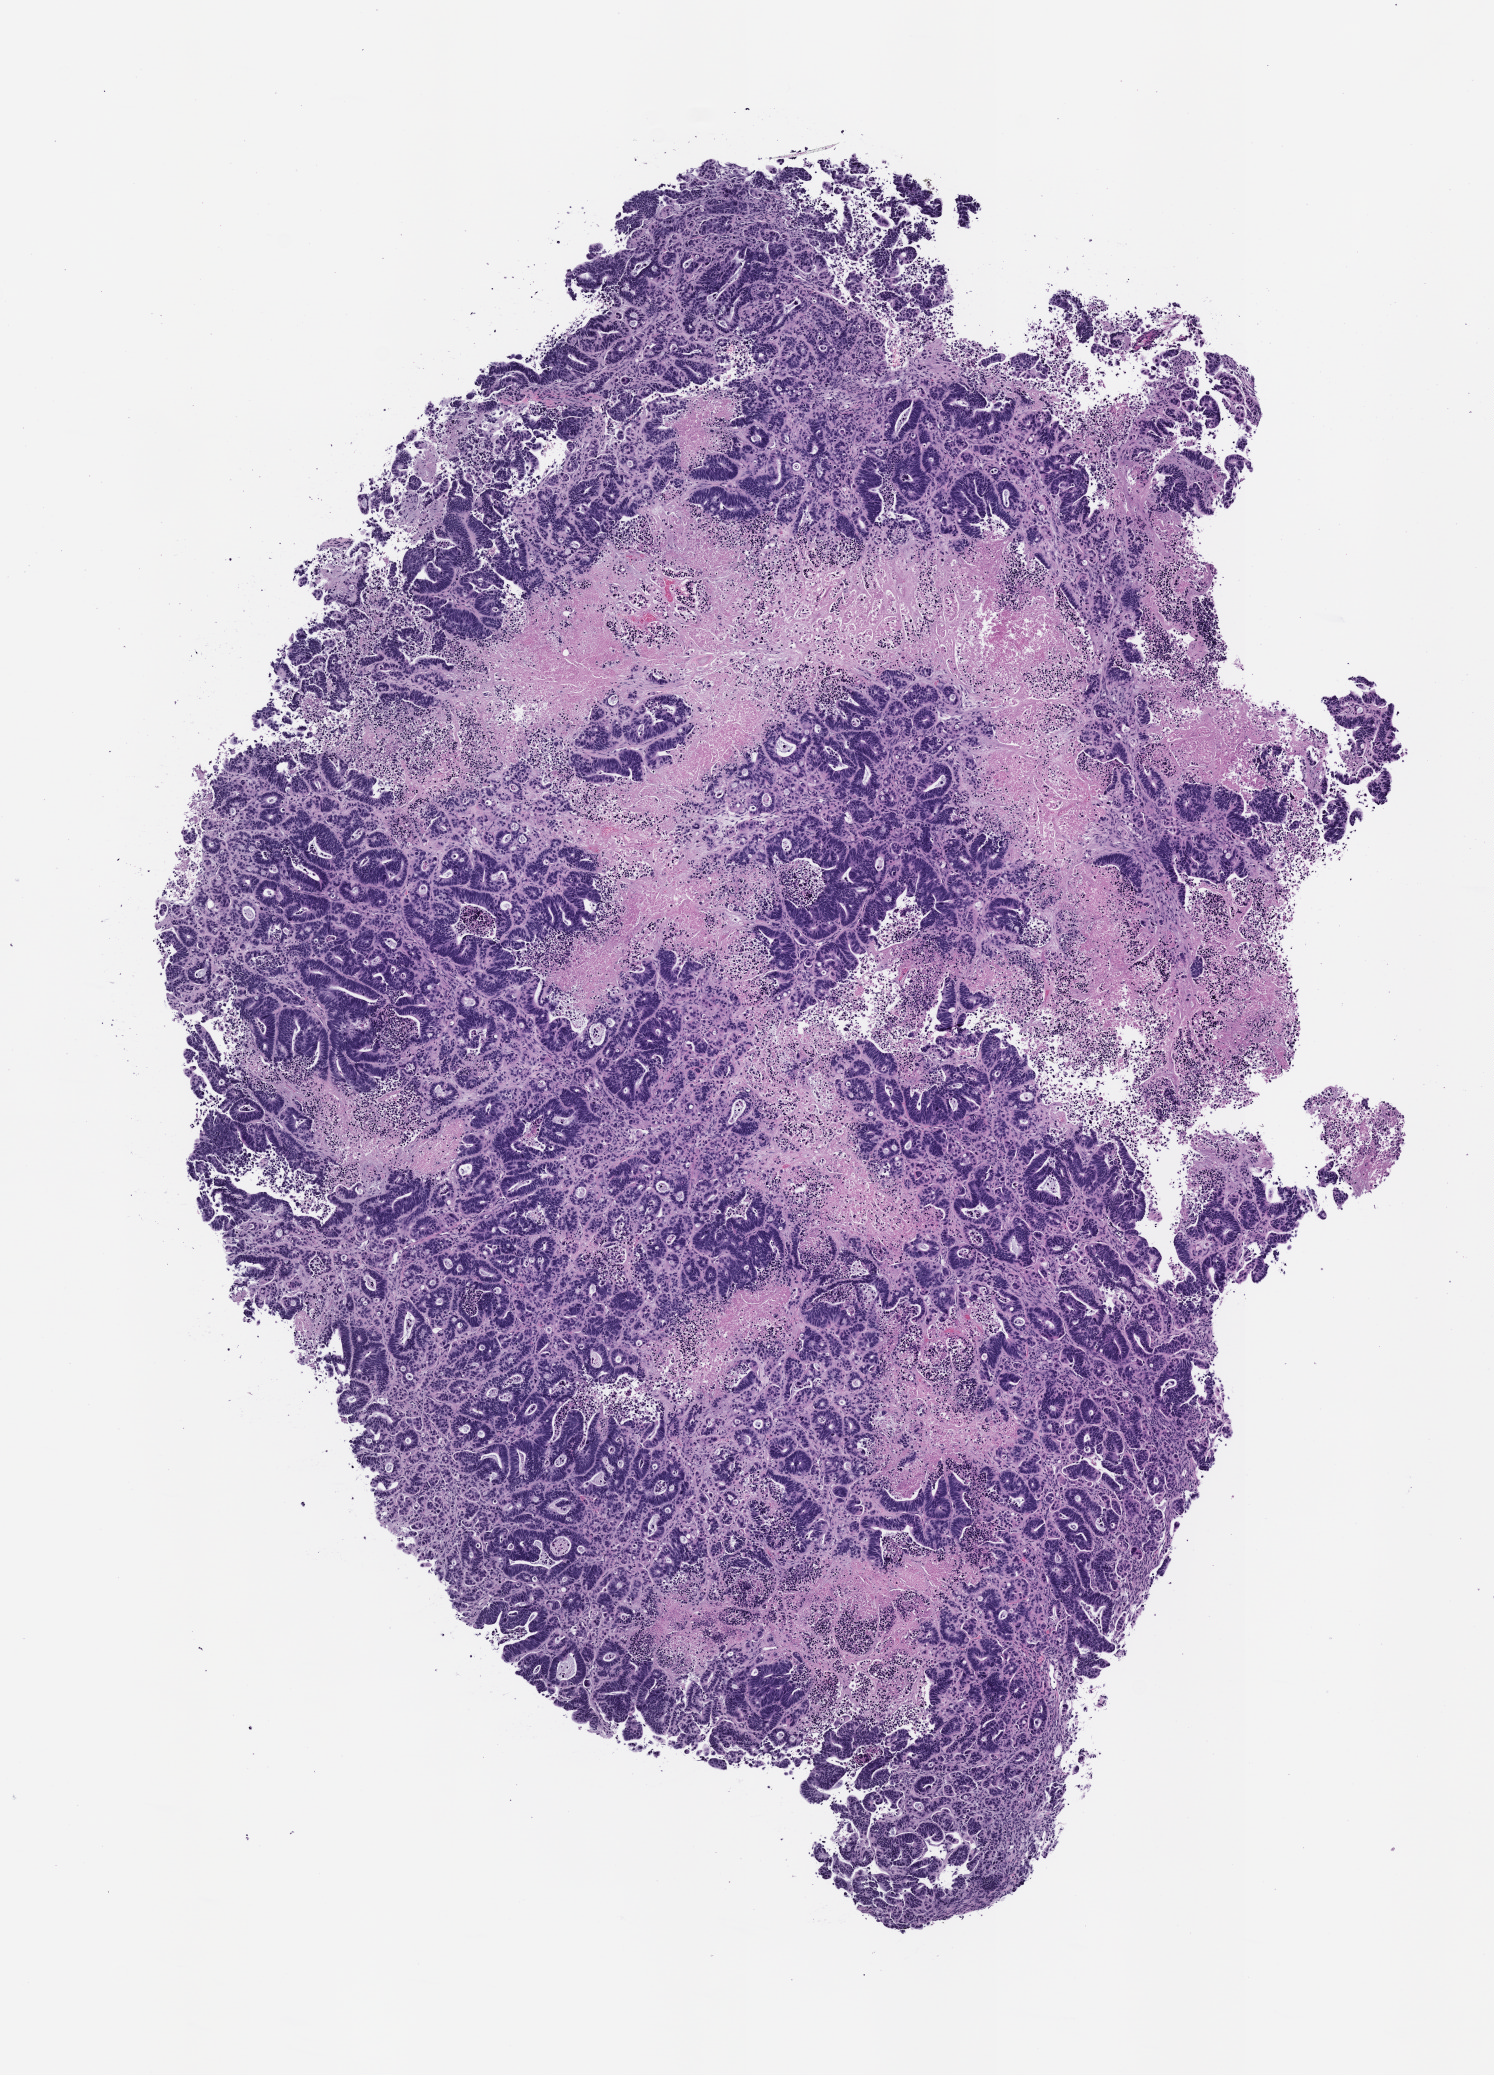
Whole-slide image, hematoxylin and eosin (H&E): patient-derived xenograft (human tumor grown in a mouse), passage 1, a low-resolution overview of the entire scanned area, about 6.0 x 8.3 mm. Formalin-fixed, paraffin-embedded (FFPE) tissue. Originating tumor site category: colon.
- originating patient diagnosis: Colon Adenocarcinoma